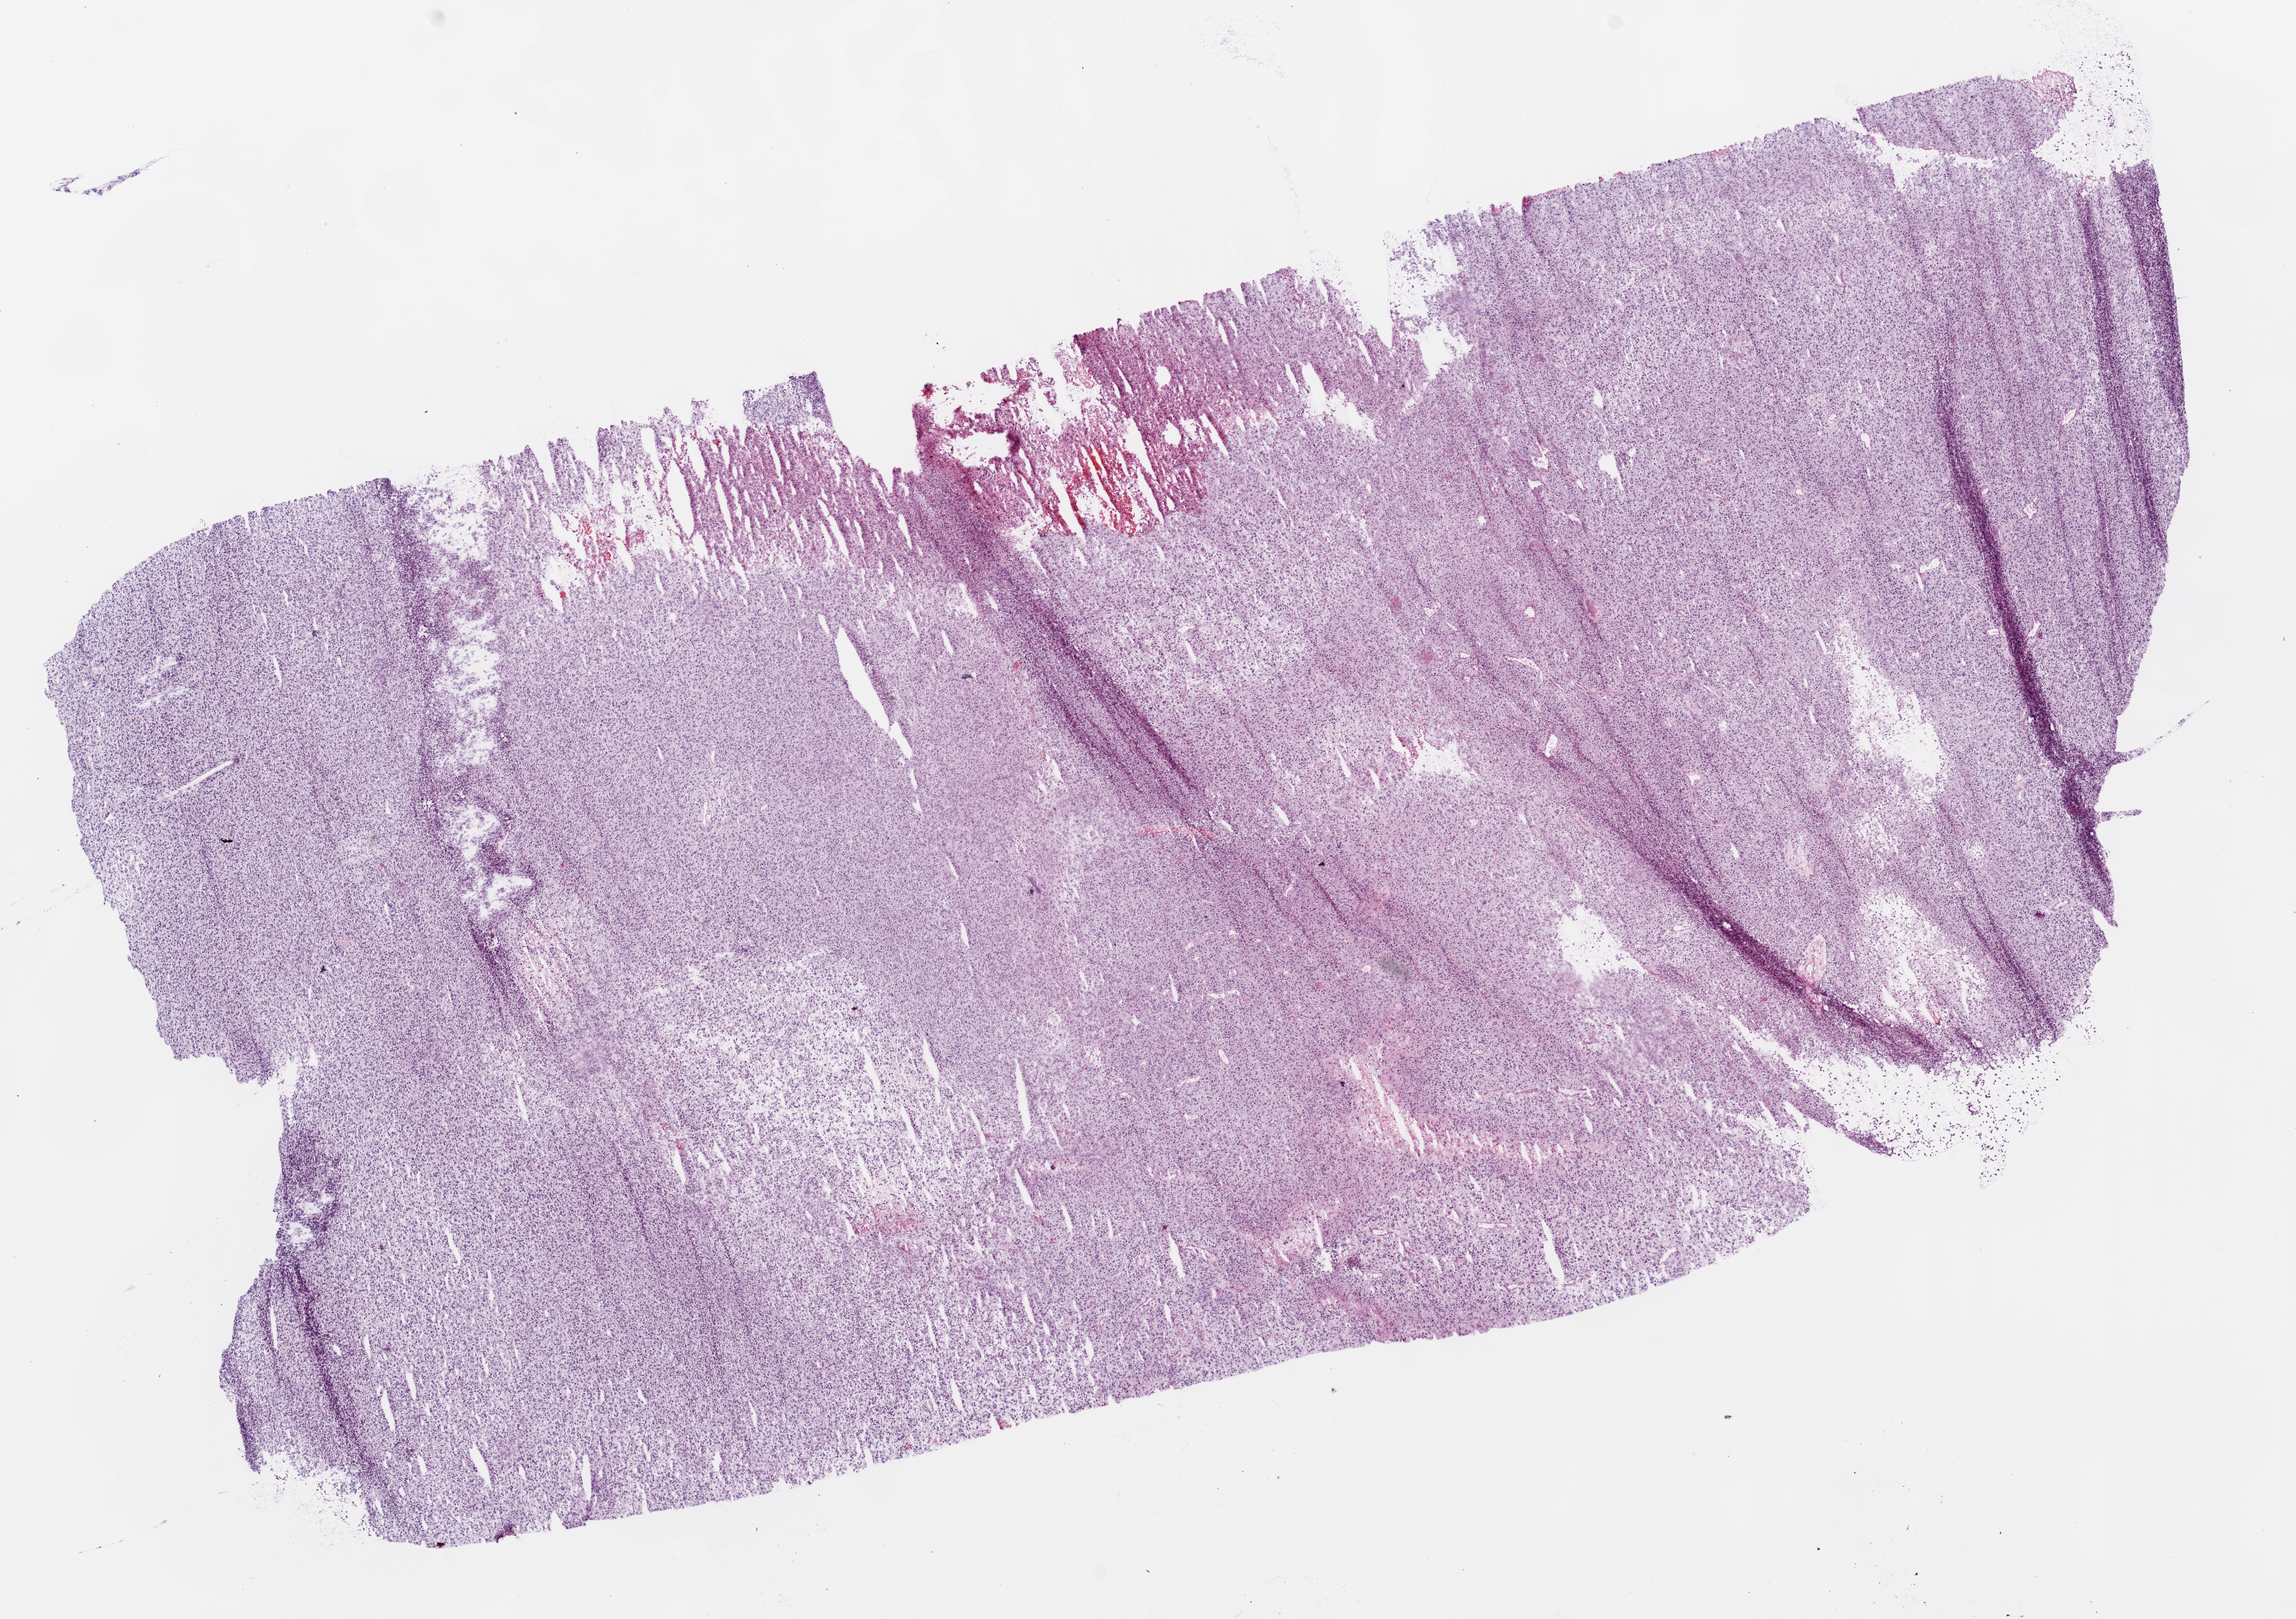
Digitized Hematoxylin and eosin (H&E) stained tissue section (whole slide), a low-resolution overview of the entire scanned area, about 13.0 x 9.2 mm, frozen section, primary tumour sample from the brain. Male patient; age at initial diagnosis 59 years. Slide review estimates, as recorded: tumour cells 95%, tumour nuclei 85%, normal cells 0%, stromal cells 0%, necrosis 5%.
• pathologic diagnosis: Glioblastoma